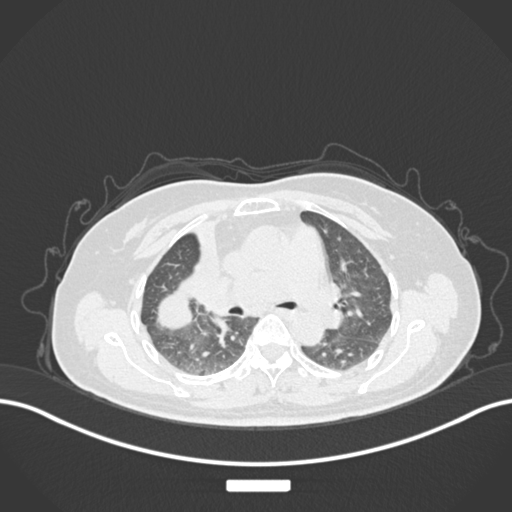
Chest CT, one axial slice; slice 93 of 177 in the series (ordered by position); reconstruction kernel B30f; 120 kVp; lung window (W 1500 / L -600 HU); 1 mm slice thickness; 512 × 512 image matrix. Female patient, age 60 years. Case-level facts recorded for this patient, not image findings: clinical TNM (as recorded): T3 N1 M1.
Annotated regions visible in this slice (rectangle marked by the reading radiologist):
- lung tumour (recorded histology: adenocarcinoma): box from (x=146, y=289) to (x=200, y=330) px